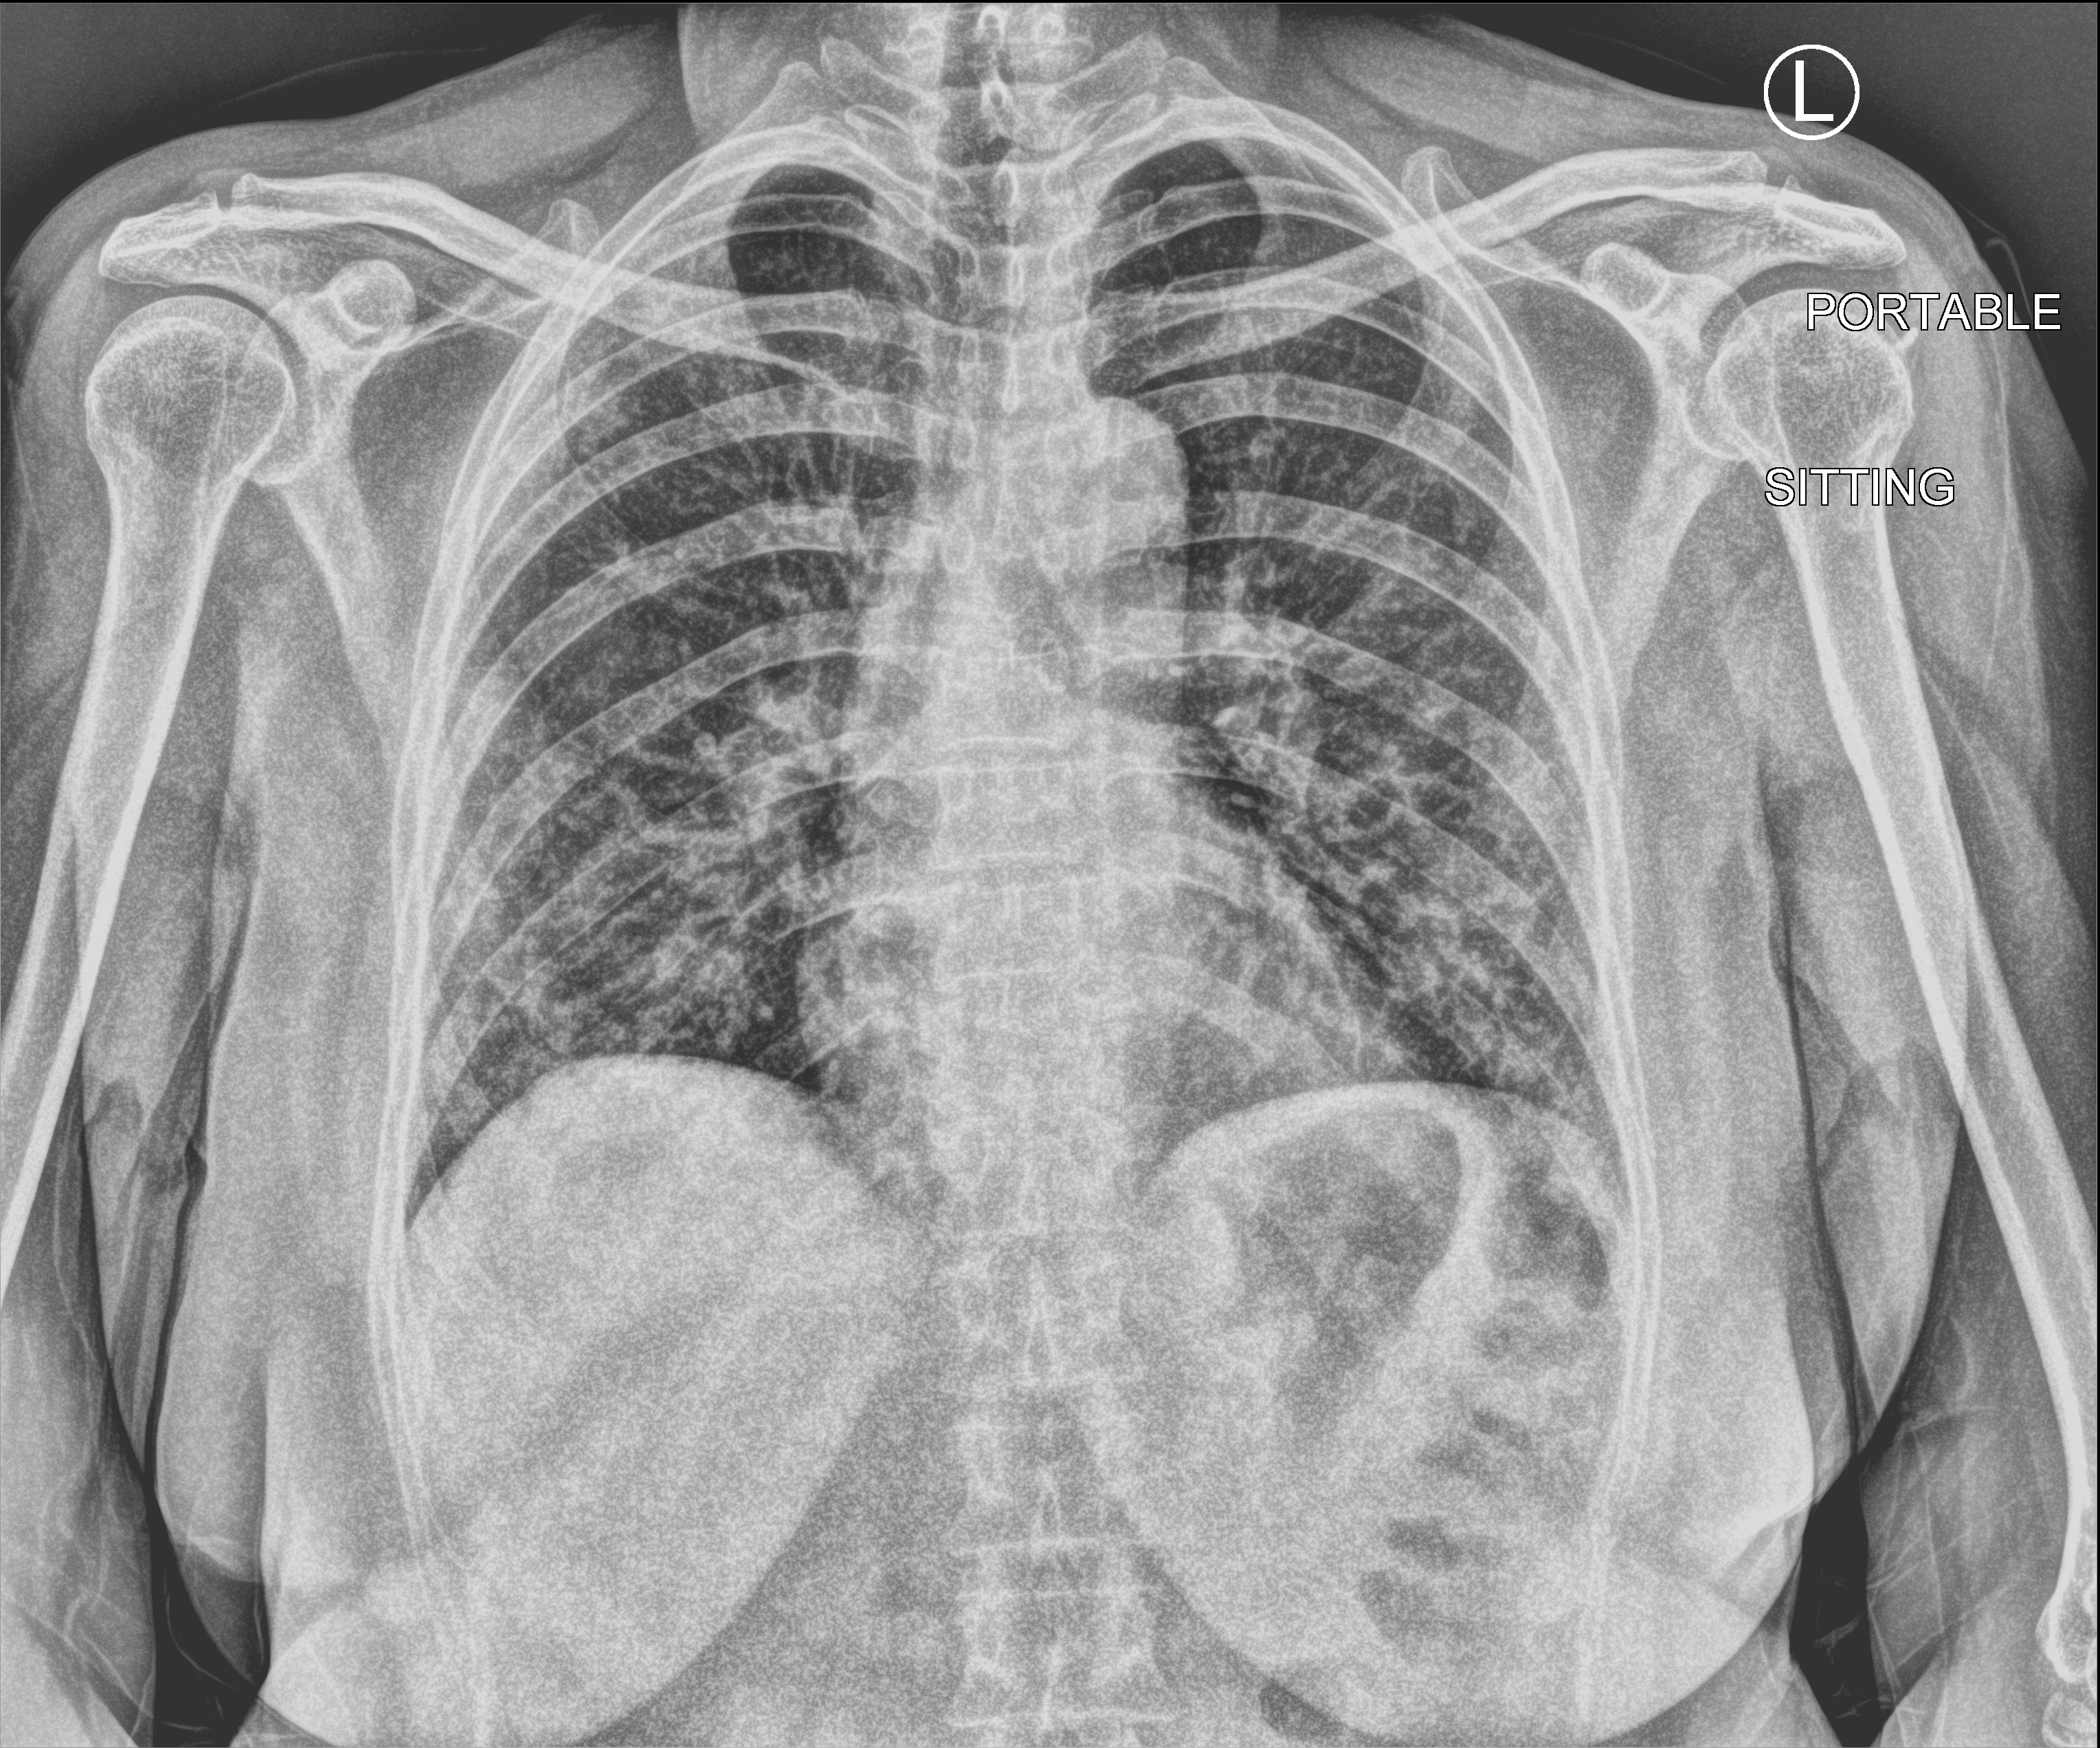
Portable chest radiograph. Patient hospitalised with COVID-19; female, aged 18–59 years.
Hospital-stay facts (about this admission, not read from this image; timing relative to this image not recorded): mechanically ventilated during this hospital stay: no.